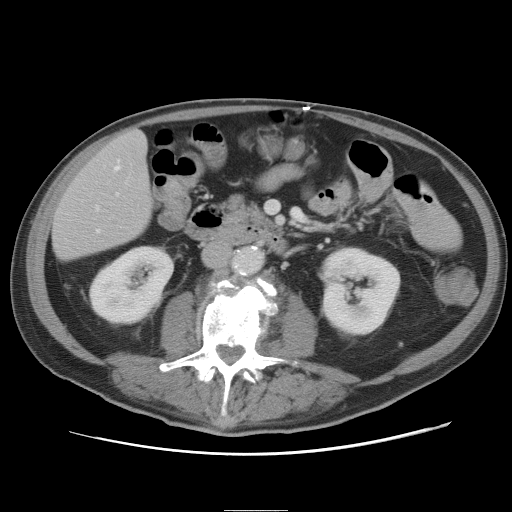
Contrast-enhanced abdominal CT, one axial slice. 120 kVp. Intravenous contrast given. Soft-tissue window (W 400 / L 40 HU). 512 × 512 image matrix. Male patient, age 69 years. Case-level facts recorded for this patient, not image findings: diagnosis: colorectal cancer liver metastases, imaged before liver resection; multiple liver metastases: no; largest metastasis: 8.5 cm; disease in both lobes: no.
Outlined on this slice (expert manual segmentation):
- hepatic veins: bounding box (x1, y1, x2, y2) in pixels: (98, 160, 120, 231)
- liver: (53, 131, 153, 261)
- planned liver remnant (the part of the liver to remain after resection): (54, 130, 153, 261)